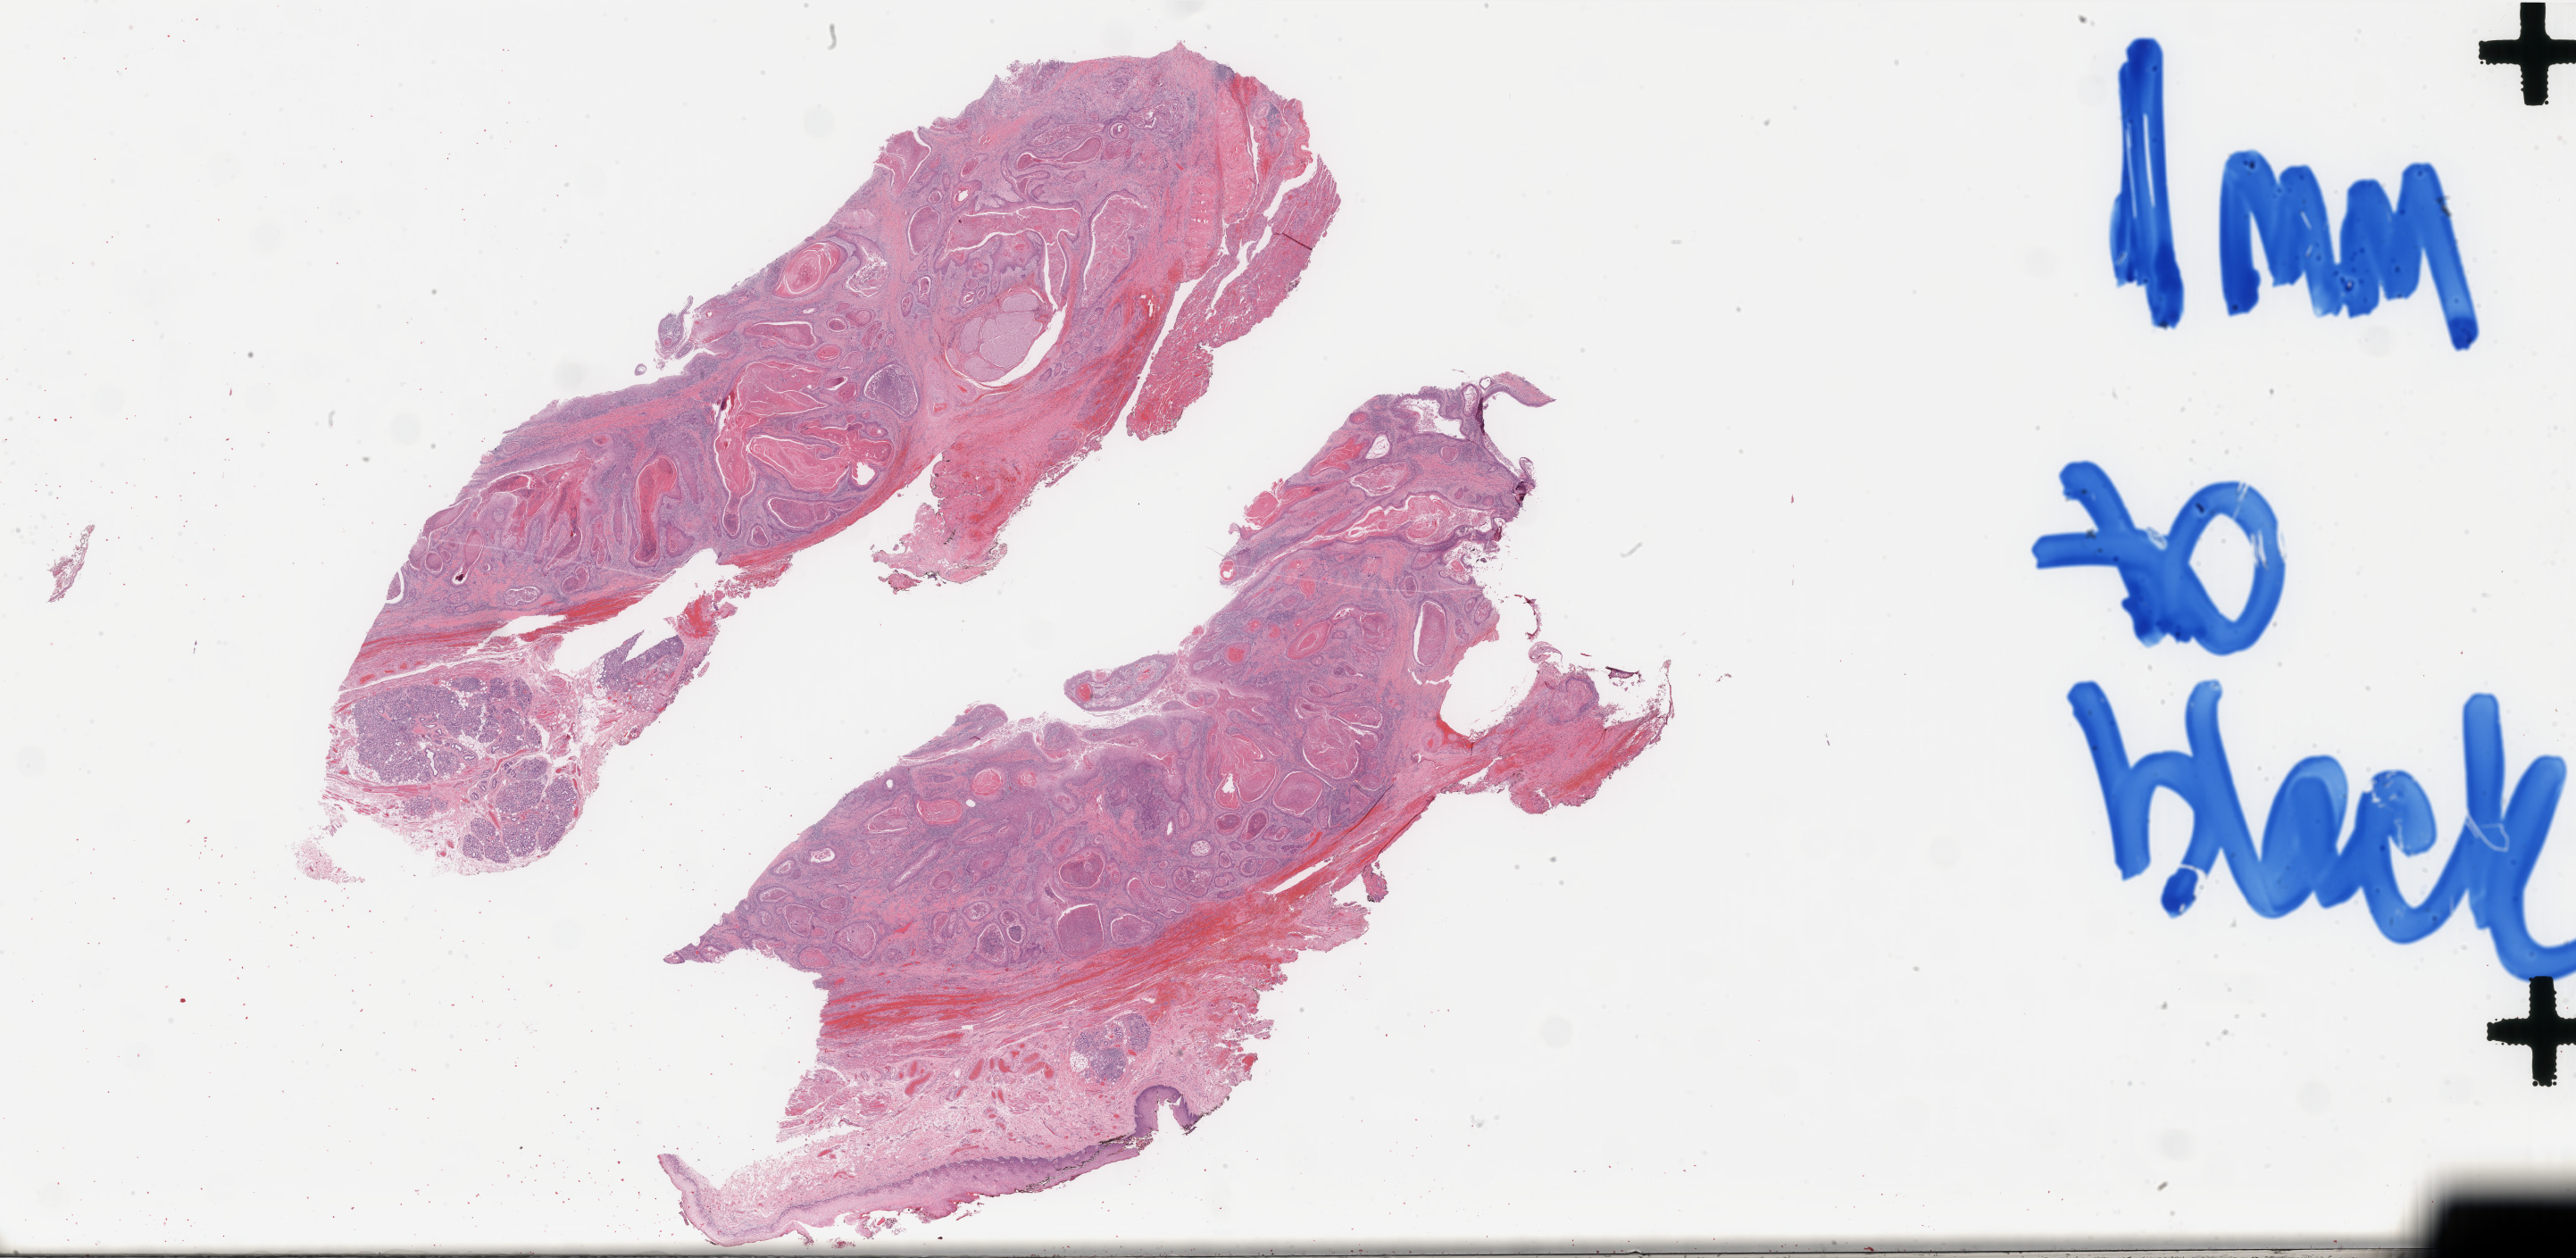
H&E-stained whole-slide image — shown as a low-resolution overview of the whole scanned area (about 45.7 x 22.3 mm, from a 40x scan), FFPE section, sample: primary tumour, head and neck. Female patient; age at initial diagnosis 80 years. Histologic grade: G2 (moderately differentiated).
* AJCC pathologic stage: IVA (7th edition)
* diagnosis: Squamous cell carcinoma, NOS (floor of mouth, NOS)
* lymph nodes positive (case pathology): 0 of 28 examined
* TNM: T4a N0 M0